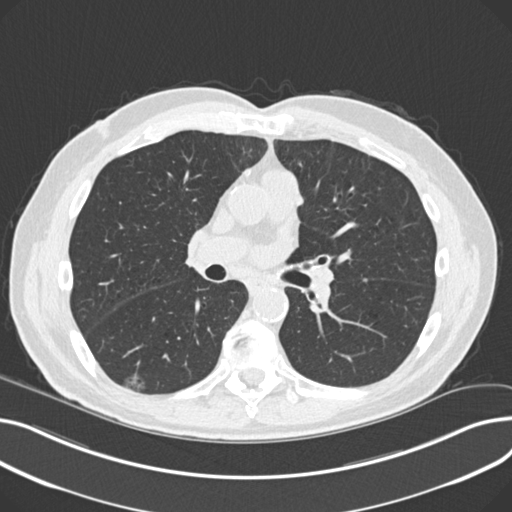
Axial slice from a low-dose chest CT screening exam. Third screening round (two years after baseline). Lung window (W 1500 / L -600 HU). 2 mm slice thickness. Standard (soft-tissue) reconstruction kernel (B30f). 512 × 512 image matrix. Male, age 68 years at enrolment. Current smoker at enrolment.
Lesion marked by an expert reader, box from (x=123, y=366) to (x=158, y=398) px. The screening reader recorded 5 non-calcified nodules or masses ≥4 mm on this exam; which of them this box marks is not recorded. Official screen result: positive, other.